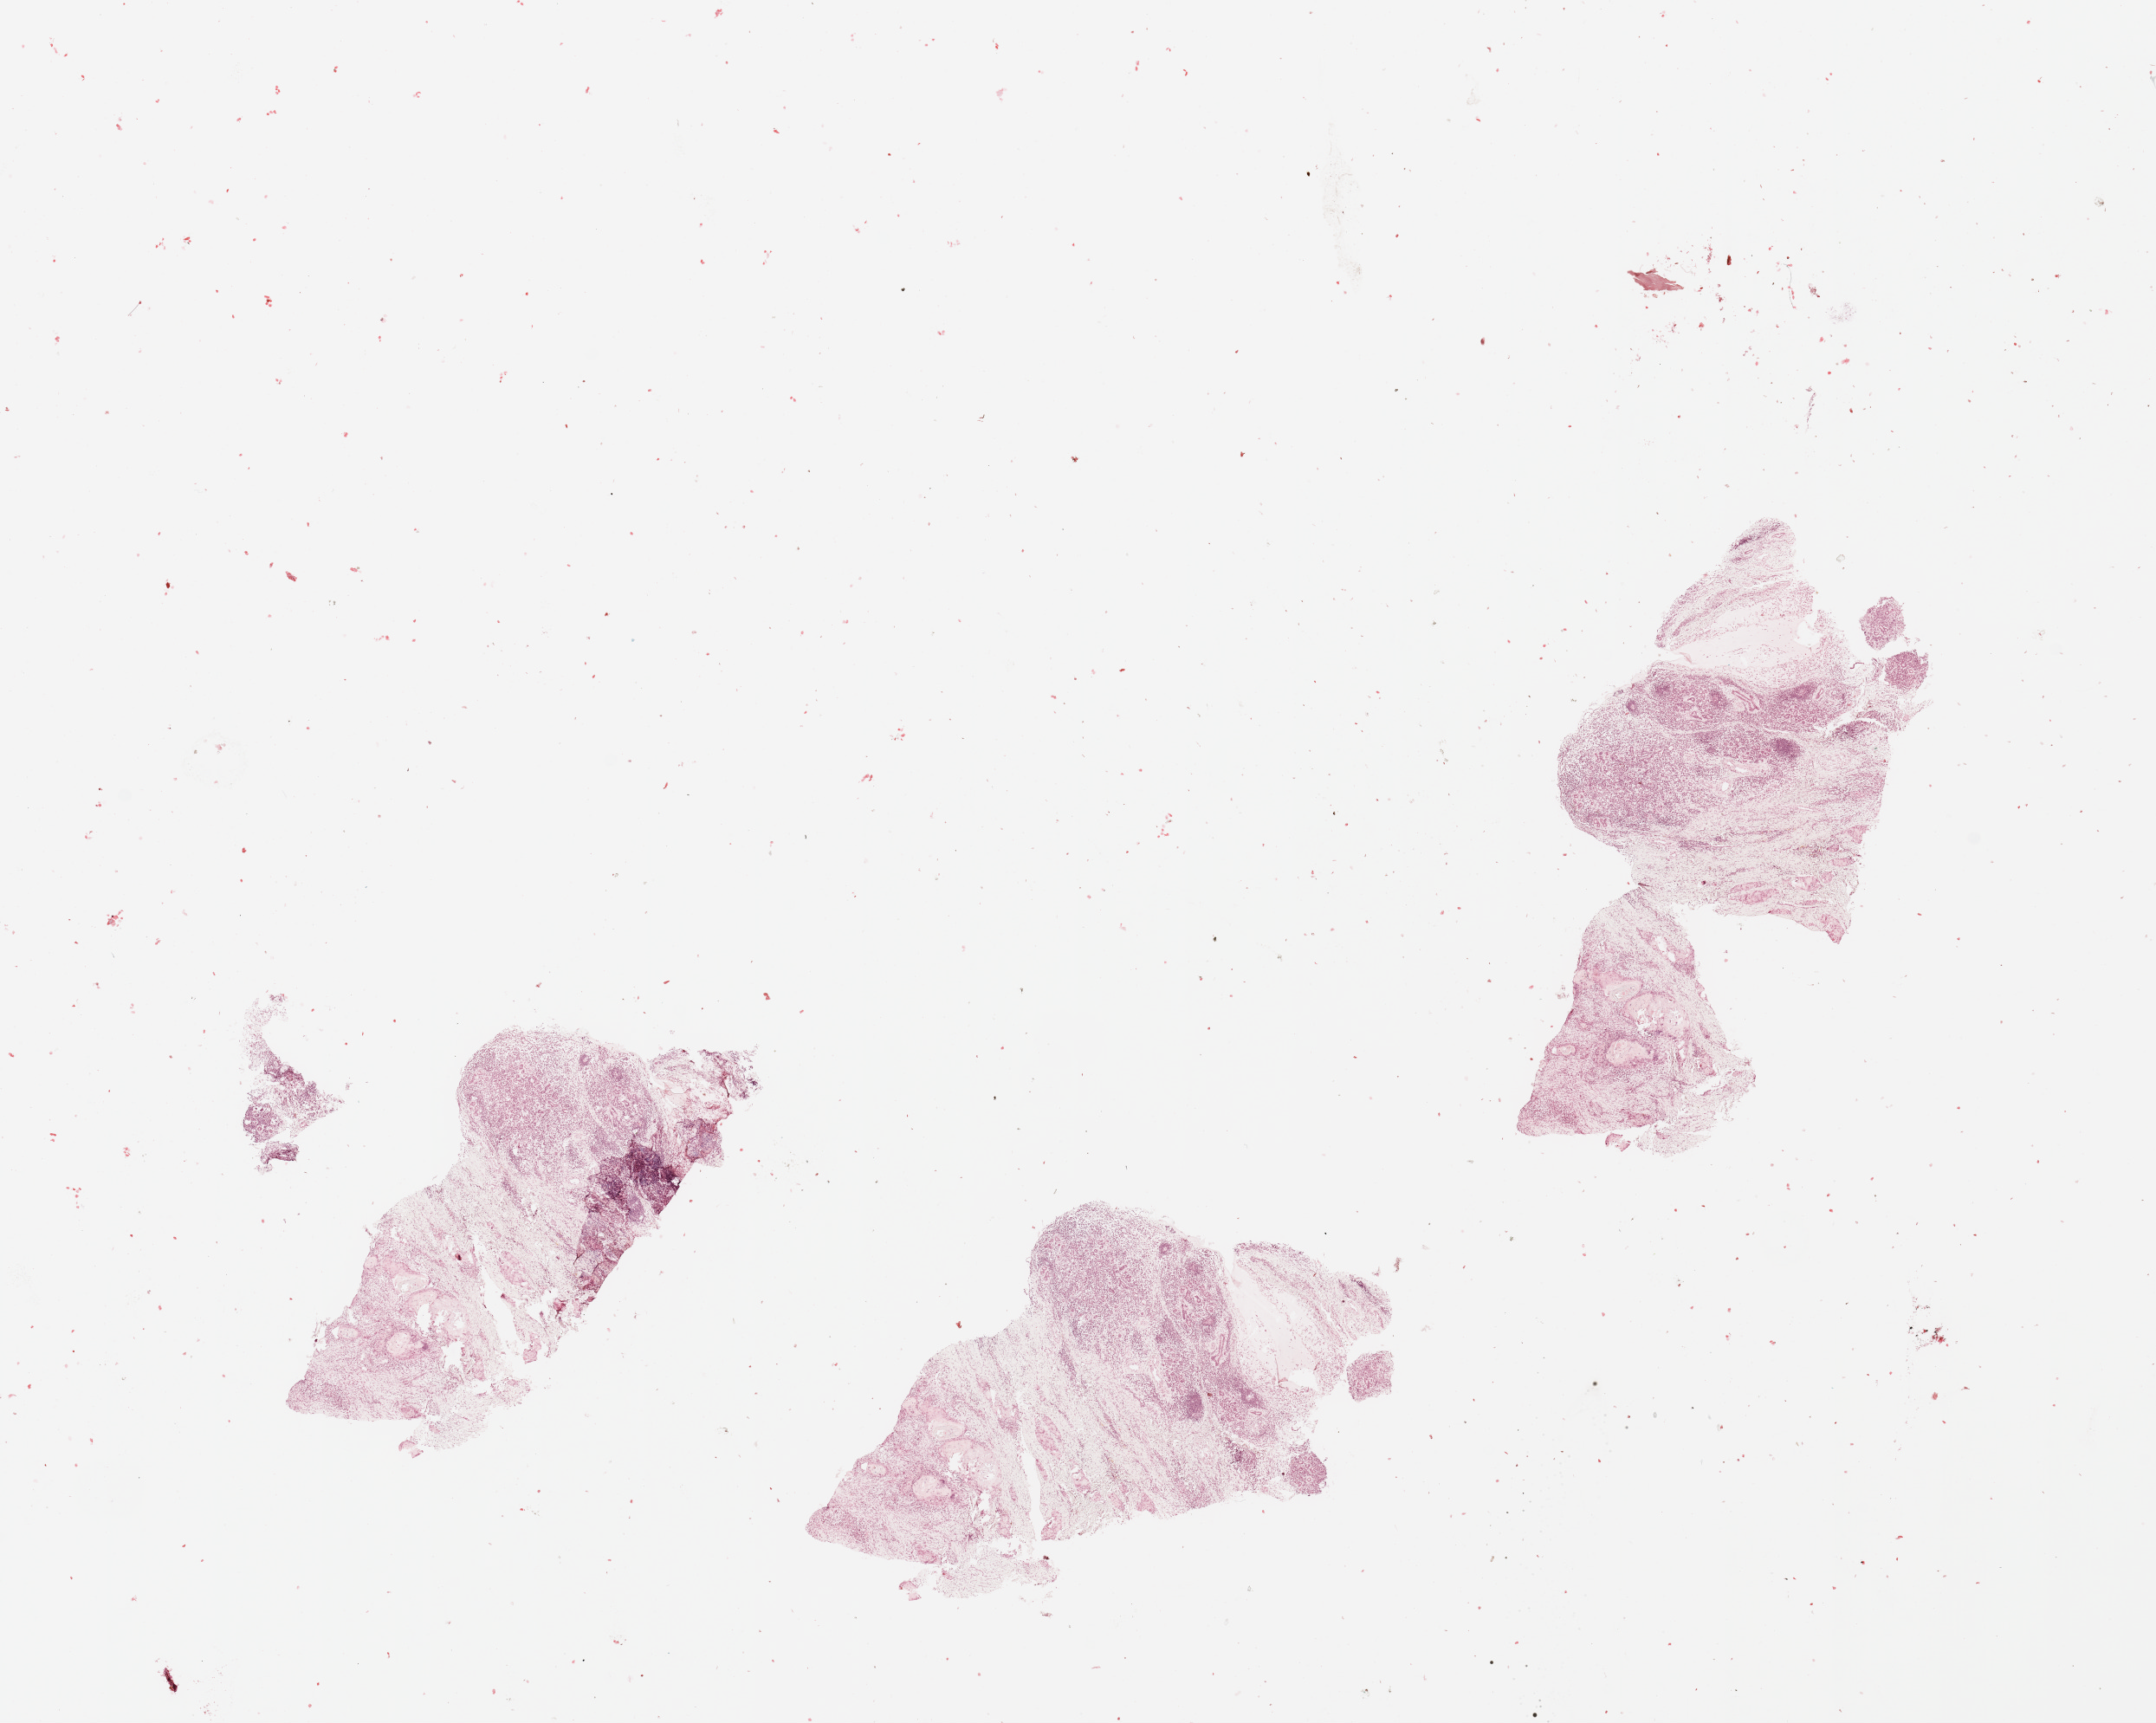
Digitized H&E tissue section (whole slide) — low-resolution overview of the scanned area, about 19.7 x 15.7 mm (slide scanned at 20x), head and neck, tissue type not recorded. Male, 64 y/o.
Patient diagnosis: Squamous cell carcinoma, NOS.